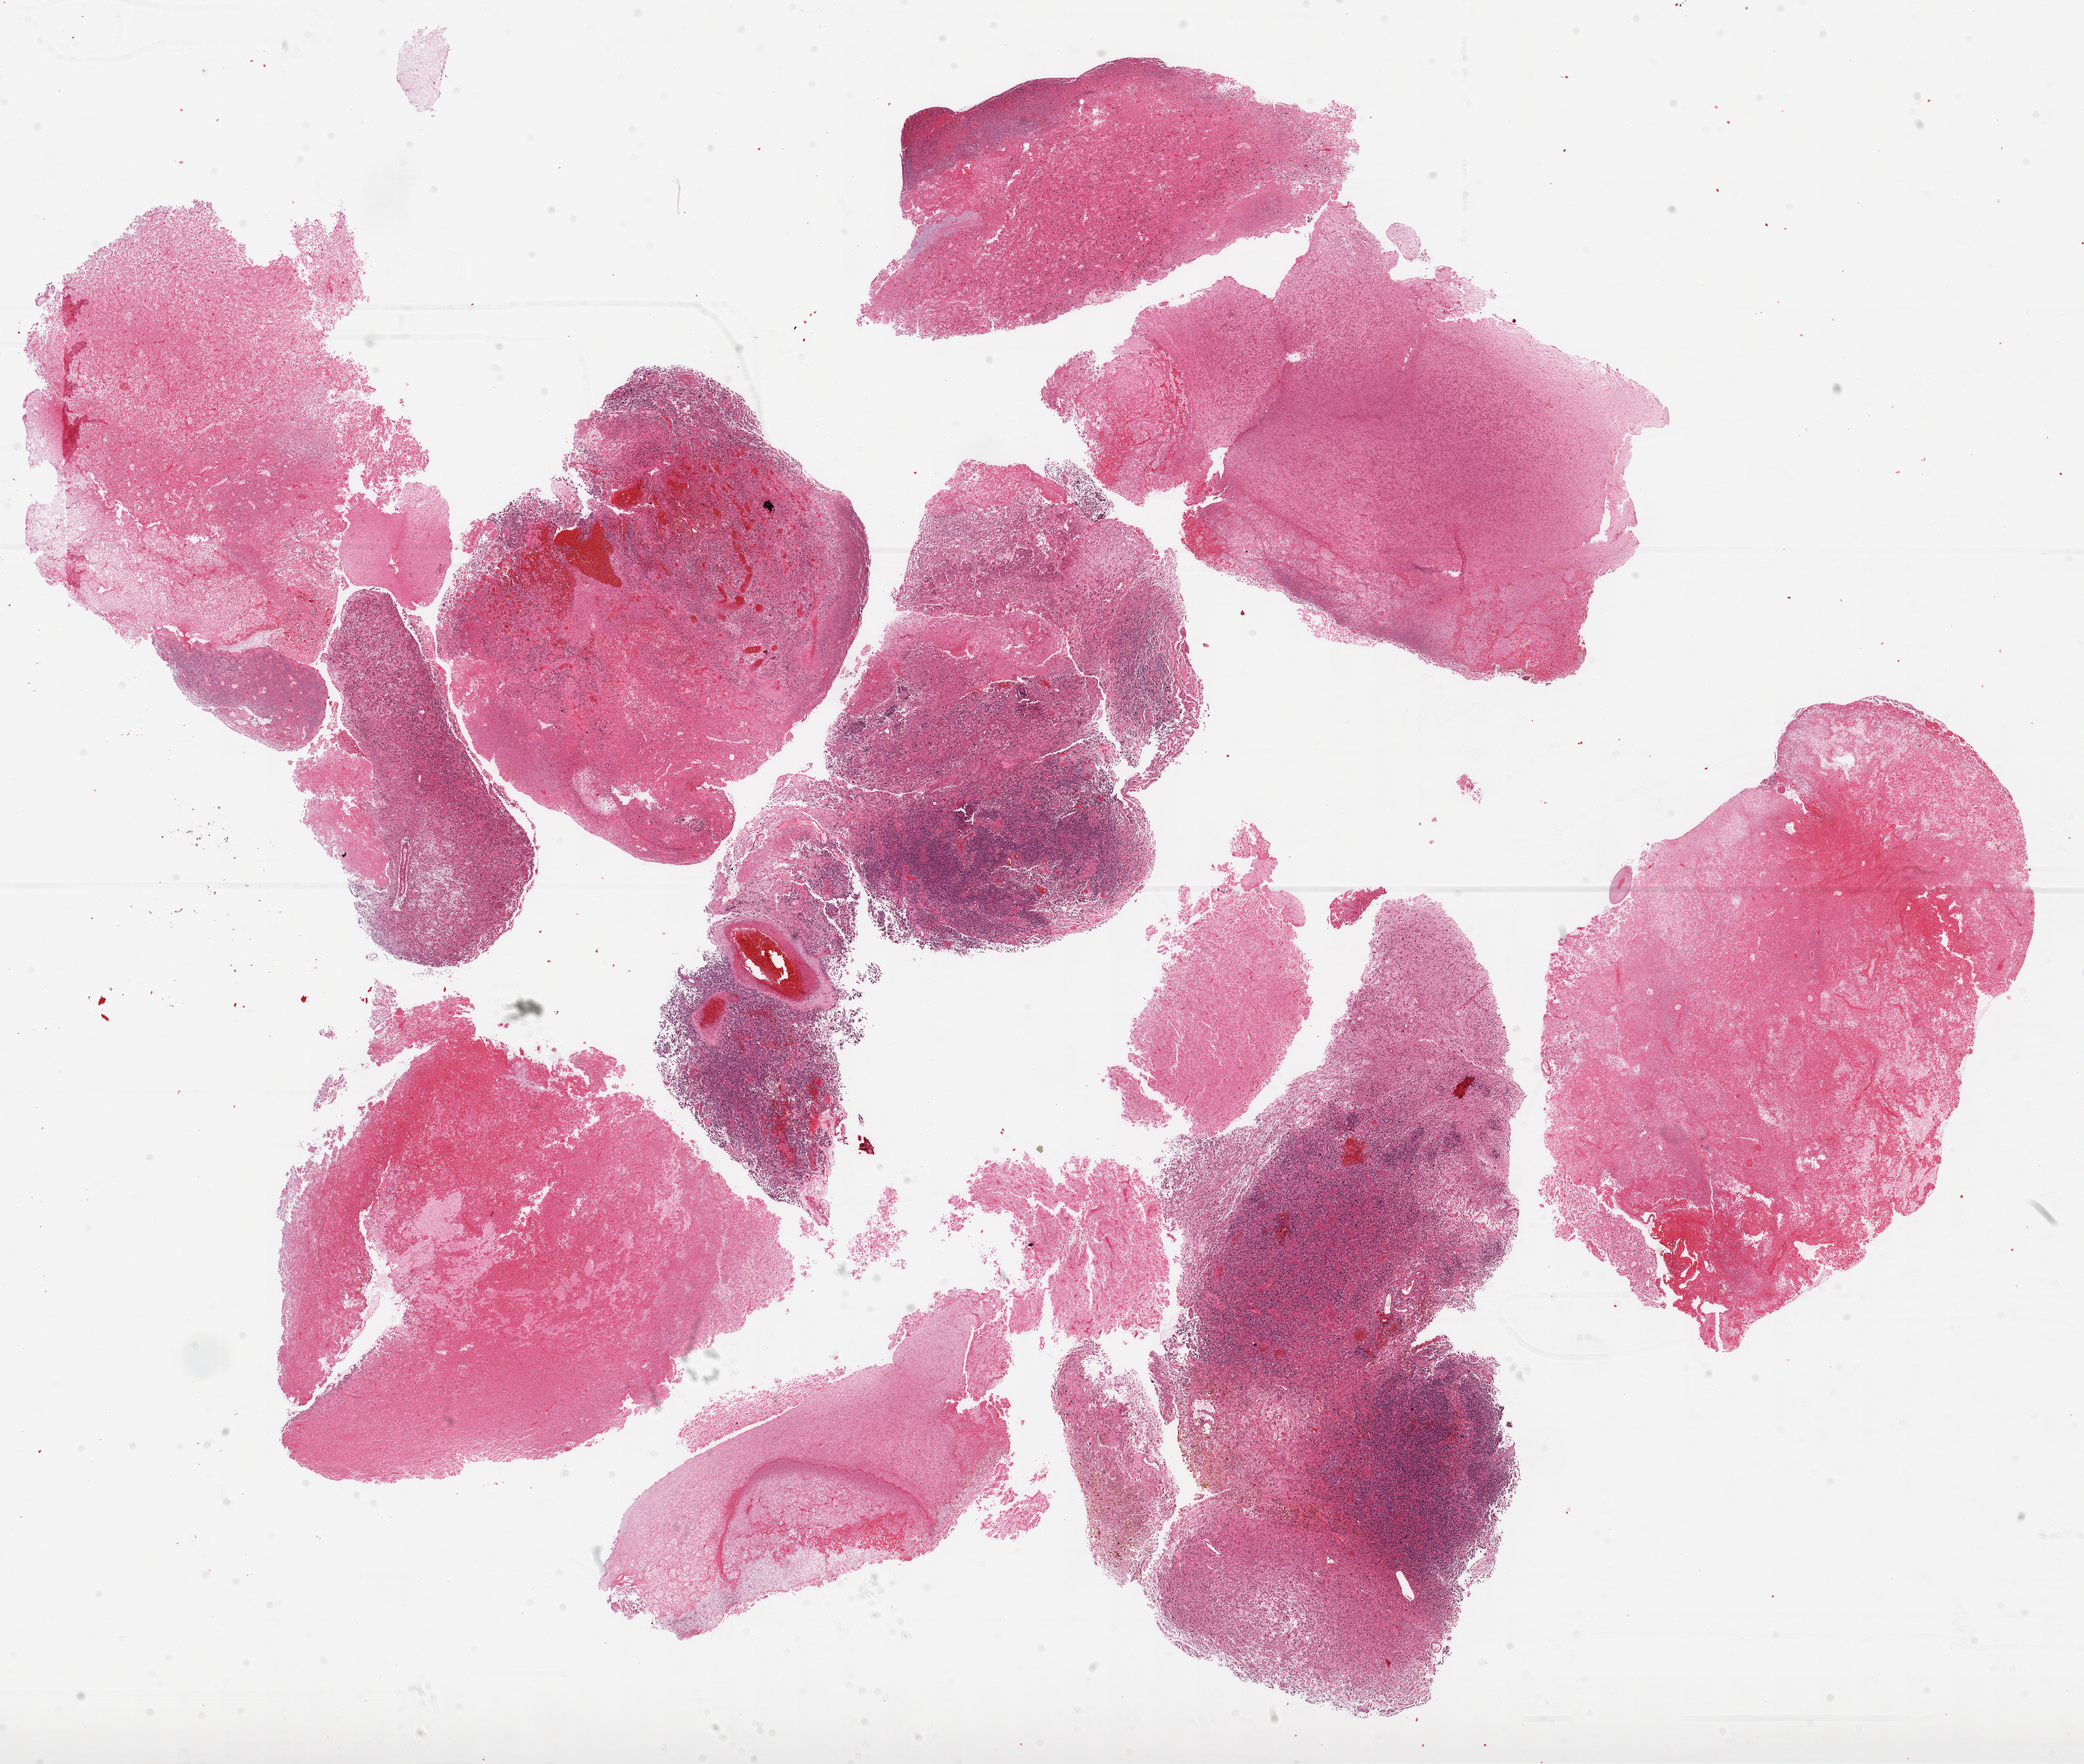
H&E-stained whole-slide image — low-resolution overview of the scanned area, about 22.7 x 19.2 mm (acquisition: 20x scan); formalin-fixed paraffin-embedded (FFPE) diagnostic section; brain, primary tumour sample. Female patient; age at initial diagnosis 69 years.
Diagnosis: Glioblastoma.